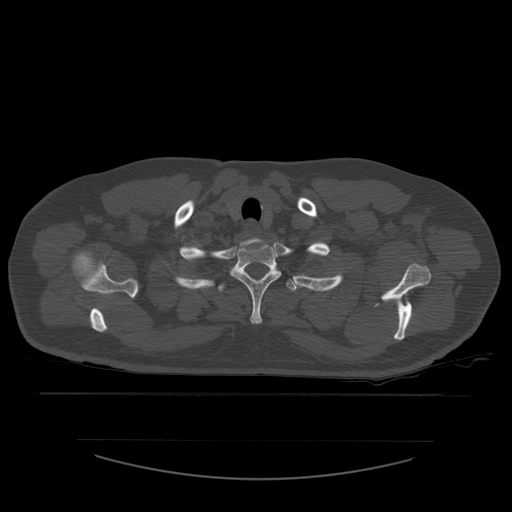
CT including the spine, one axial slice; slice 466 of 532 in the series (ordered by position); 120 kVp; bone window (W 1800 / L 400 HU); 1.25 mm slice thickness; 512 × 512 image matrix, field of view 441 × 441 mm. Patient age 44 years. Case-level facts recorded for this patient, not image findings: primary cancer: soft tissue sarcoma.
Structures marked on this image (semi-automatic segmentation, software-assisted and operator-edited):
- T1 vertebra: bounding box <231,242,282,324> (left, top, right, bottom; pixels)
- T2 vertebra: <219,279,313,292>